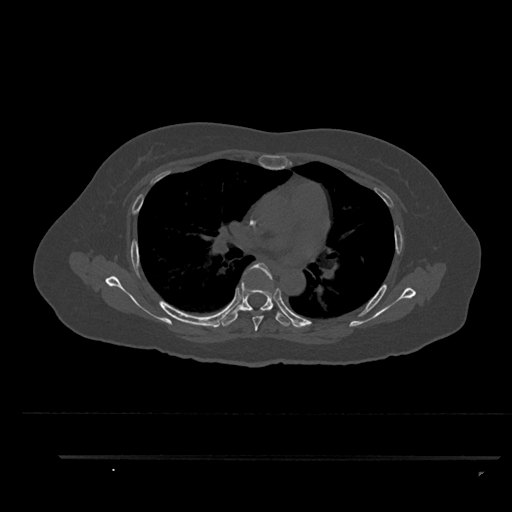
CT including the spine, one axial slice; position 578 of 797 along the scan axis; reconstruction kernel Br40s/3; bone window (W 1800 / L 400 HU); 0.5 mm slice thickness; 512 × 512 image matrix, field of view 408 × 408 mm. Patient: female, 44 years. Case-level facts recorded for this patient, not image findings: primary cancer: renal; vertebrae with lytic lesions (as recorded): L1.
Outlined on this slice (semi-automatic segmentation, software-assisted and operator-edited):
- T5 vertebra: box from (x=247, y=263) to (x=273, y=331) px
- T6 vertebra: (x=221, y=280)–(x=295, y=327)